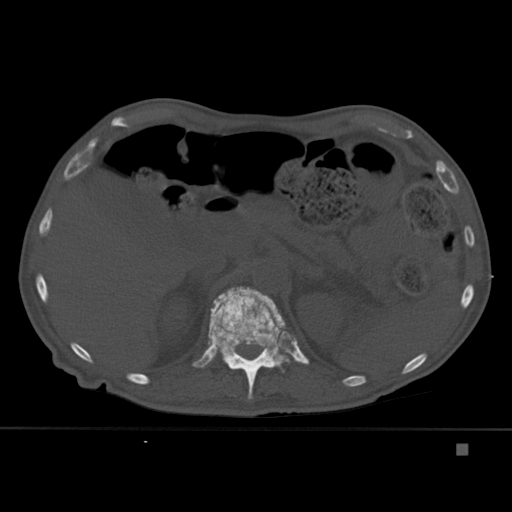
CT including the spine, one axial slice. Slice 199 of 451 in the series (ordered by position). Bone window (W 1800 / L 400 HU). 512 × 512 image matrix, field of view 378 × 378 mm. Patient: male, 75 years. From the clinical record (not read from this slice): primary cancer: prostate.
Structures marked on this image (semi-automatically segmented with operator editing):
- T12 vertebra: bounding box [x1, y1, x2, y2] px = [208, 286, 290, 400]